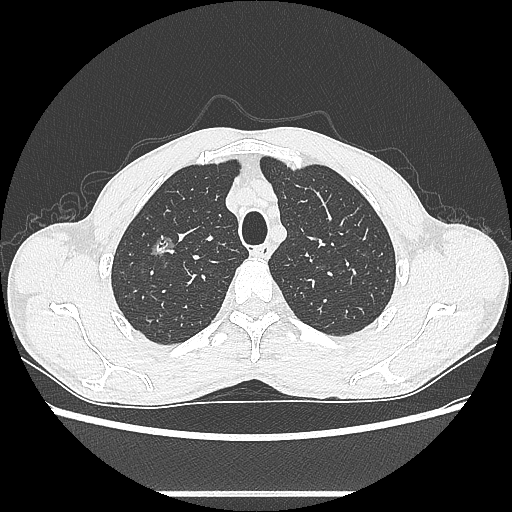
Chest CT, one axial slice; position 484 of 601 along the scan axis; reconstruction kernel LUNG; lung window (W 1500 / L -600 HU); 0.62 mm slice thickness; 512 × 512 image matrix, field of view 357 × 357 mm. Male patient, age 54 years. From the clinical record (not read from this slice): clinical TNM (as recorded): T1a N0 M0.
Annotated regions visible in this slice (rectangle marked by the reading radiologist):
- lung tumour (recorded histology: adenocarcinoma): bounding box <142,225,176,268> (left, top, right, bottom; pixels)